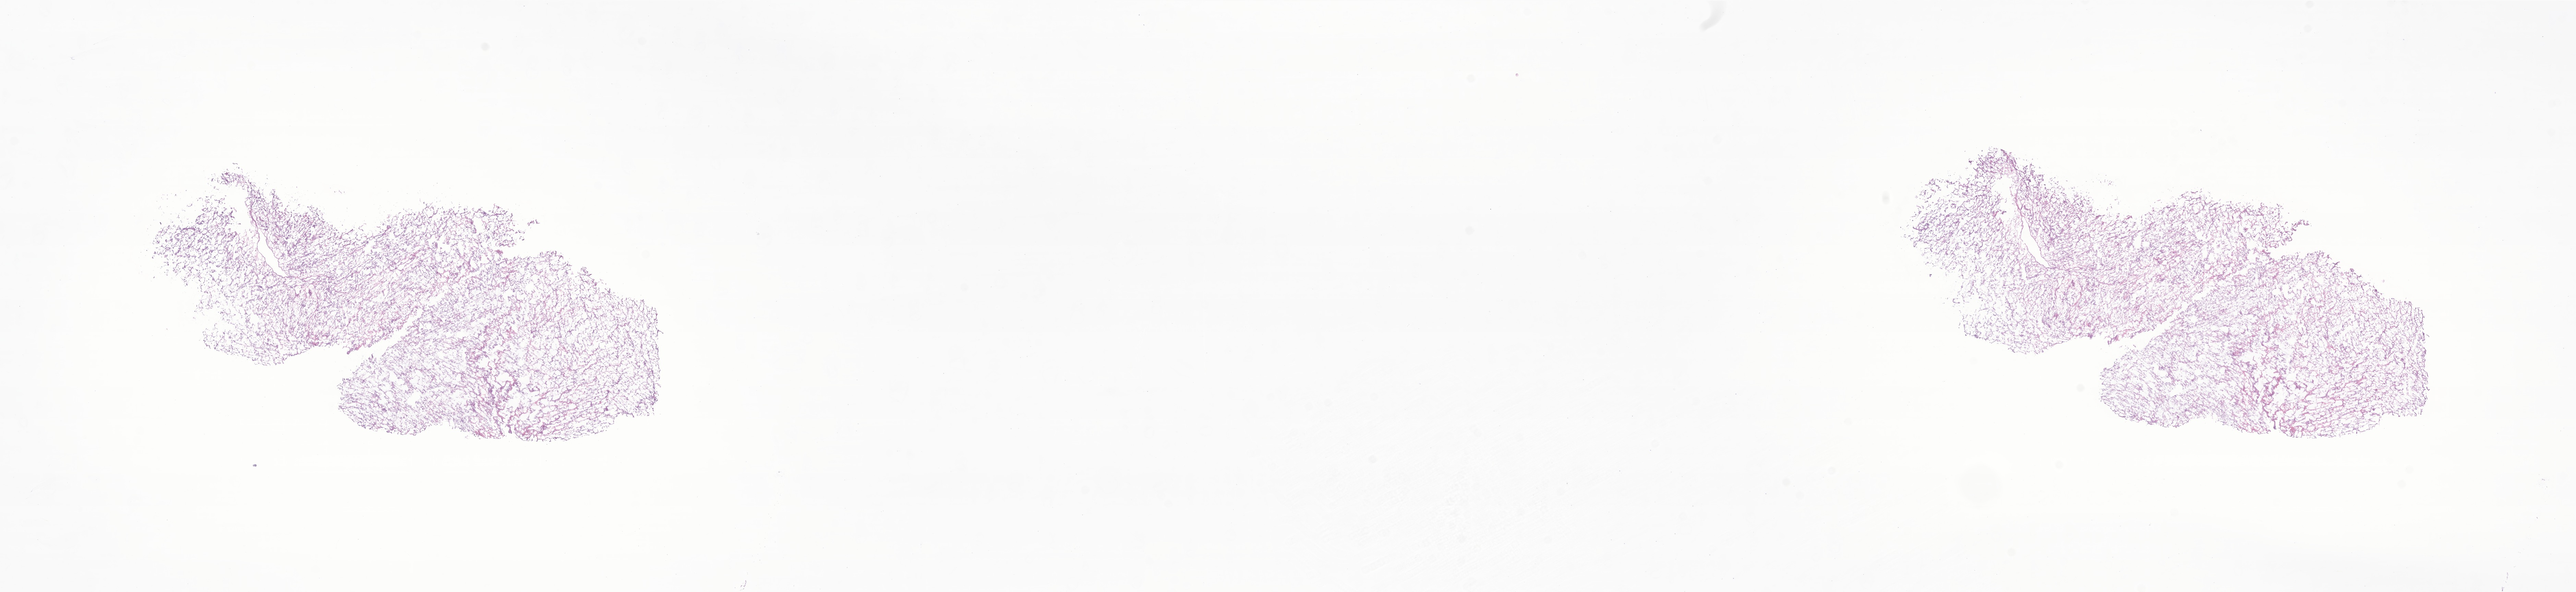
Haematoxylin and eosin whole-slide image of tumor tissue from the testis — whole scanned area (about 31.7 x 7.3 mm) shown as a low-resolution overview. Cryosection (OCT / tissue freezing medium). Patient male; age 150 months (12 years 6 months).
Diagnosis: Embryonal rhabdomyosarcoma, NOS.